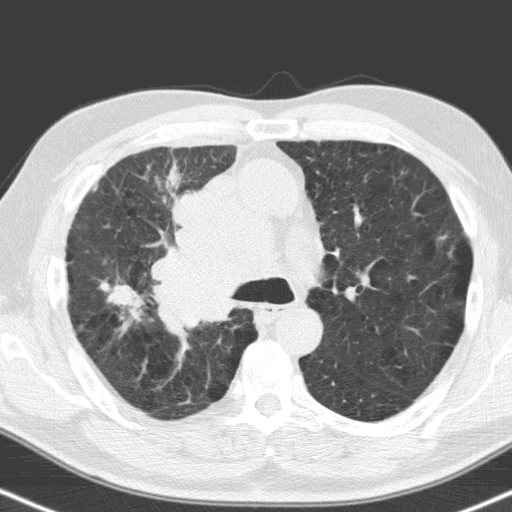
Axial slice from a low-dose chest CT screening exam, first (baseline) screen, lung window (W 1500 / L -600 HU), standard (soft-tissue) reconstruction kernel (C), 120 kVp. Male, age 71 years at enrolment. Former smoker at enrolment.
- Lesion marked by an expert reader, bounding box [x1, y1, x2, y2] px = [85, 271, 156, 340].
- The screening reader recorded 2 non-calcified nodules or masses ≥4 mm on this exam (right upper lobe, right upper lobe); which of them this box marks is not recorded.
- Participant outcome: lung cancer diagnosed 31 days after this screen — small cell carcinoma, NOS, right upper lobe, stage IV (AJCC 6th edition), 40 mm at pathology.